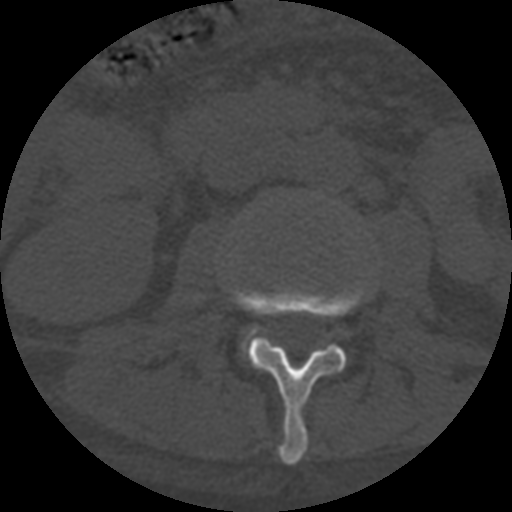
CT including the spine, one axial slice. Slice 251 of 708 in the series (ordered by position). Reconstruction kernel STANDARD. One of 3 acquisitions stored at this slice position. Bone window (W 1800 / L 400 HU). 1.25 mm slice thickness. 512 × 512 image matrix, field of view 160 × 160 mm. Patient age 55 years. Case-level facts recorded for this patient, not image findings: primary cancer: colon; vertebrae with lytic lesions (as recorded): T12, L1, L5.
Structures marked on this image (semi-automatic segmentation, software-assisted and operator-edited):
- L2 vertebra: bounding box <231,285,365,465> (left, top, right, bottom; pixels)